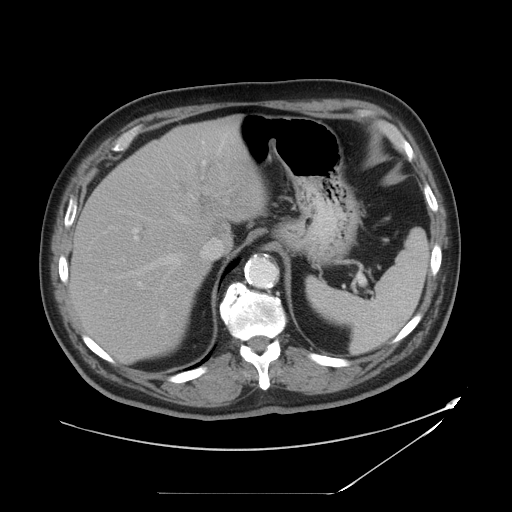
Contrast-enhanced abdominal CT, one axial slice; position 33 of 49 along the scan axis; reconstruction kernel STANDARD; 120 kVp; intravenous contrast given; soft-tissue window (W 400 / L 40 HU); 512 × 512 image matrix, field of view 461 × 461 mm. Male patient, age 72 years. Case-level facts recorded for this patient, not image findings: diagnosis: colorectal cancer liver metastases, imaged before liver resection; multiple liver metastases: no; largest metastasis: 2.5 cm.
Annotated regions visible in this slice (outlined manually by an expert reader):
- hepatic veins: box from (x=126, y=164) to (x=218, y=277) px
- liver: (x=71, y=120)–(x=263, y=361)
- planned liver remnant (the part of the liver to remain after resection): (x=71, y=173)–(x=206, y=361)
- portal vein (with intrahepatic branches): (x=132, y=132)–(x=229, y=289)
- liver metastasis: (x=199, y=184)–(x=248, y=212)